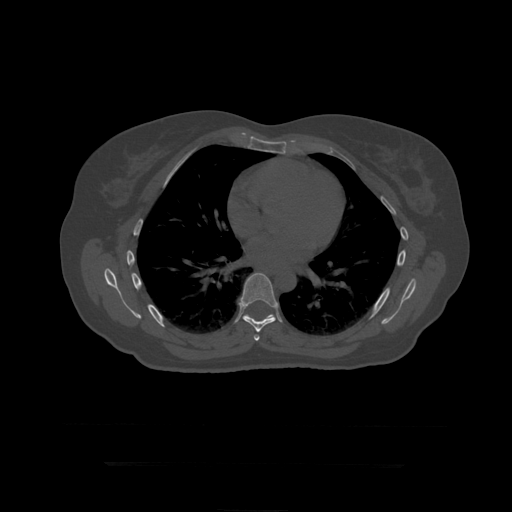
CT including the spine, one axial slice. Slice 278 of 399 in the series (ordered by position). Reconstruction kernel STANDARD. Bone window (W 1800 / L 400 HU). 1.25 mm slice thickness. 512 × 512 image matrix, field of view 450 × 450 mm. Patient age 41 years. Case-level facts recorded for this patient, not image findings: primary cancer: breast.
Structures marked on this image (semi-automatic segmentation, software-assisted and operator-edited):
- T7 vertebra: box from (x=254, y=335) to (x=260, y=341) px
- T8 vertebra: (x=241, y=273)–(x=276, y=333)
- T9 vertebra: (x=246, y=315)–(x=251, y=318)